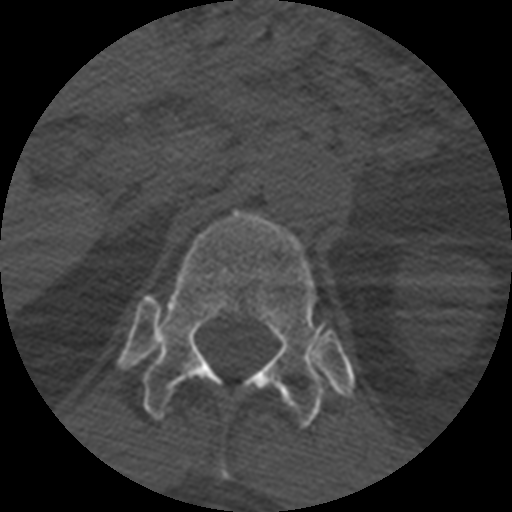
CT including the spine, one axial slice; slice 389 of 399 in the series (ordered by position); bone window (W 1800 / L 400 HU); 1.25 mm slice thickness; 512 × 512 image matrix, field of view 160 × 160 mm. Patient age 71 years. Case-level facts recorded for this patient, not image findings: primary cancer: prostate.
Structures marked on this image (semi-automatic segmentation, software-assisted and operator-edited):
- T11 vertebra: bounding box (x1, y1, x2, y2) in pixels: (218, 460, 230, 481)
- T12 vertebra: (141, 210, 329, 430)